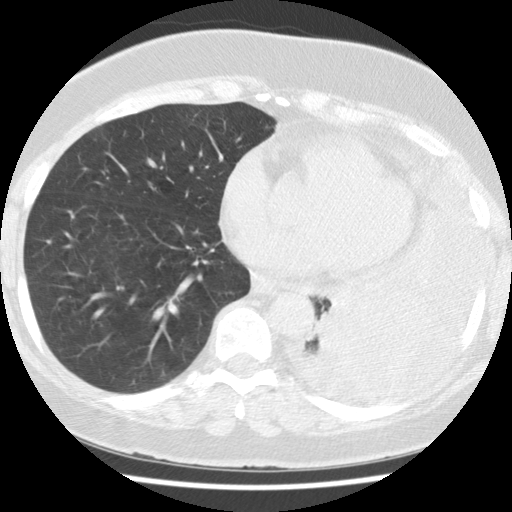
Low-dose screening chest CT, axial slice, baseline annual screen, lung window (W 1500 / L -600 HU), 2.5 mm slice thickness, 120 kVp, slice 71 of 114 in the series. Female, age 65 years at enrolment. Current smoker at enrolment.
Lesion marked by an expert reader, bounding box <315,281,439,387> (left, top, right, bottom; pixels). Reader record for this screening exam (exam-level; its link to the box is not recorded): non-calcified nodule or mass ≥4 mm, left lower lobe, 74 × 48 mm, spiculated (stellate) margins, soft tissue attenuation. Official screen result: positive, change unspecified: nodule(s) >= 4 mm or enlarging nodule(s), mass(es), or other non-specific abnormalities suspicious for lung cancer. Participant outcome: lung cancer diagnosed 13 days after this screen — adenocarcinoma, NOS, left lower lobe, stage IV (AJCC 6th edition), 74 mm at pathology.